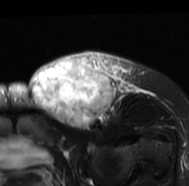
MRI of an extremity soft-tissue mass, one axial slice; position 46 of 77 along the scan axis; T2-weighted fat-saturated; MR volume resampled by the dataset authors to the PET/CT grid (not the native acquisition matrix); 3.27 mm slice thickness; 189 × 186 image matrix, field of view 185 × 182 mm. Female patient. From the clinical record (not read from this slice): histological type: leiomyosarcoma; grade: high; site of the primary tumour: groin.
Structures marked on this image (expert contour drawn on MRI and transferred to this co-registered scan by the dataset authors):
- gross tumour volume including surrounding oedema: box from (x=28, y=50) to (x=150, y=130) px
- gross tumour volume (mass): (x=29, y=56)–(x=114, y=130)